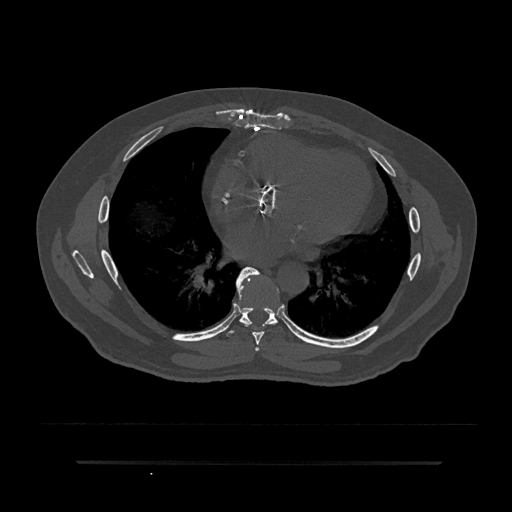
CT including the spine, one axial slice. Position 455 of 797 along the scan axis. Reconstruction kernel Br40s/3. Bone window (W 1800 / L 400 HU). 0.5 mm slice thickness. 512 × 512 image matrix, field of view 464 × 464 mm. Male patient, age 59 years. Case-level facts recorded for this patient, not image findings: primary cancer: bile ducts; vertebrae with lytic lesions (as recorded): T10.
Outlined on this slice (semi-automatic segmentation, software-assisted and operator-edited):
- T6 vertebra: bounding box <255,347,259,352> (left, top, right, bottom; pixels)
- T7 vertebra: <236,267,279,345>
- T8 vertebra: <224,278,296,336>